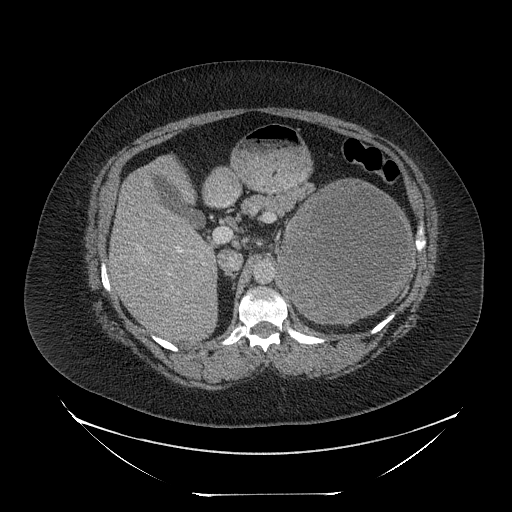
Contrast-enhanced abdominal CT, one axial slice. Position 146 of 205 along the scan axis. Reconstruction kernel STANDARD. 120 kVp. Intravenous contrast given. Soft-tissue window (W 400 / L 40 HU). 2.5 mm slice thickness. 512 × 512 image matrix, field of view 500 × 500 mm. Female patient, age 53 years. Case-level facts recorded for this patient, not image findings: diagnosis: adrenocortical carcinoma; tumour side: left adrenal; tumour size at pathology: 17 cm; Ki-67 index: 20 %.
Structures marked on this image (semi-automatically segmented with operator editing):
- mass: bounding box [x1, y1, x2, y2] px = [282, 182, 412, 320]